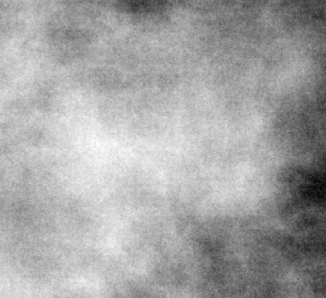
Cropped region of a digitized screen-film mammogram centred on a radiologist-marked abnormality; left breast; CC view; BI-RADS breast density category 3 (scale 1–4).
- Marked abnormality: mass, shape lobulated, margins circumscribed / ill defined; BI-RADS assessment category 3; subtlety rating 3 on a 1 (subtle) to 5 (obvious) scale; pathology (as recorded): malignant.